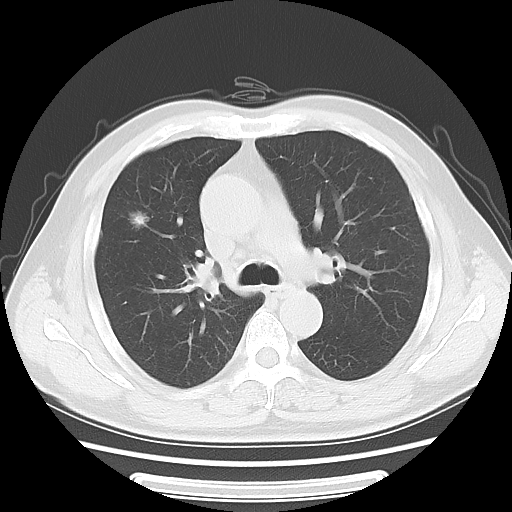
Chest CT, one axial slice; position 39 of 63 along the scan axis; reconstruction kernel LUNG; 120 kVp; lung window (W 1500 / L -600 HU); 5 mm slice thickness; 512 × 512 image matrix. Patient: male, 63 years. From the clinical record (not read from this slice): clinical TNM (as recorded): T1c N0 M0; histopathological grade: G2-3.
Annotated regions visible in this slice (rectangle marked by the reading radiologist):
- lung tumour (recorded histology: adenocarcinoma): bounding box (x1, y1, x2, y2) in pixels: (122, 200, 149, 241)